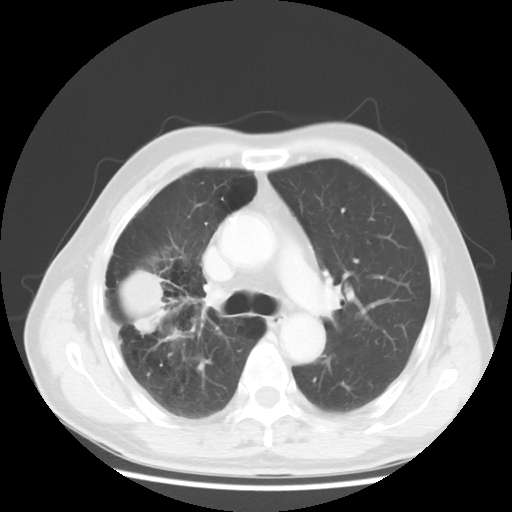
Chest CT, one axial slice. Position 31 of 50 along the scan axis. Lung window (W 1500 / L -600 HU). 5 mm slice thickness. 512 × 512 image matrix, field of view 360 × 360 mm. Male patient, age 69 years. From the clinical record (not read from this slice): clinical TNM (as recorded): T3 N0 M0; histopathological grade: G3.
Annotated regions visible in this slice (rectangle marked by the reading radiologist):
- lung tumour (recorded histology: adenocarcinoma): bounding box [x1, y1, x2, y2] px = [111, 264, 174, 339]